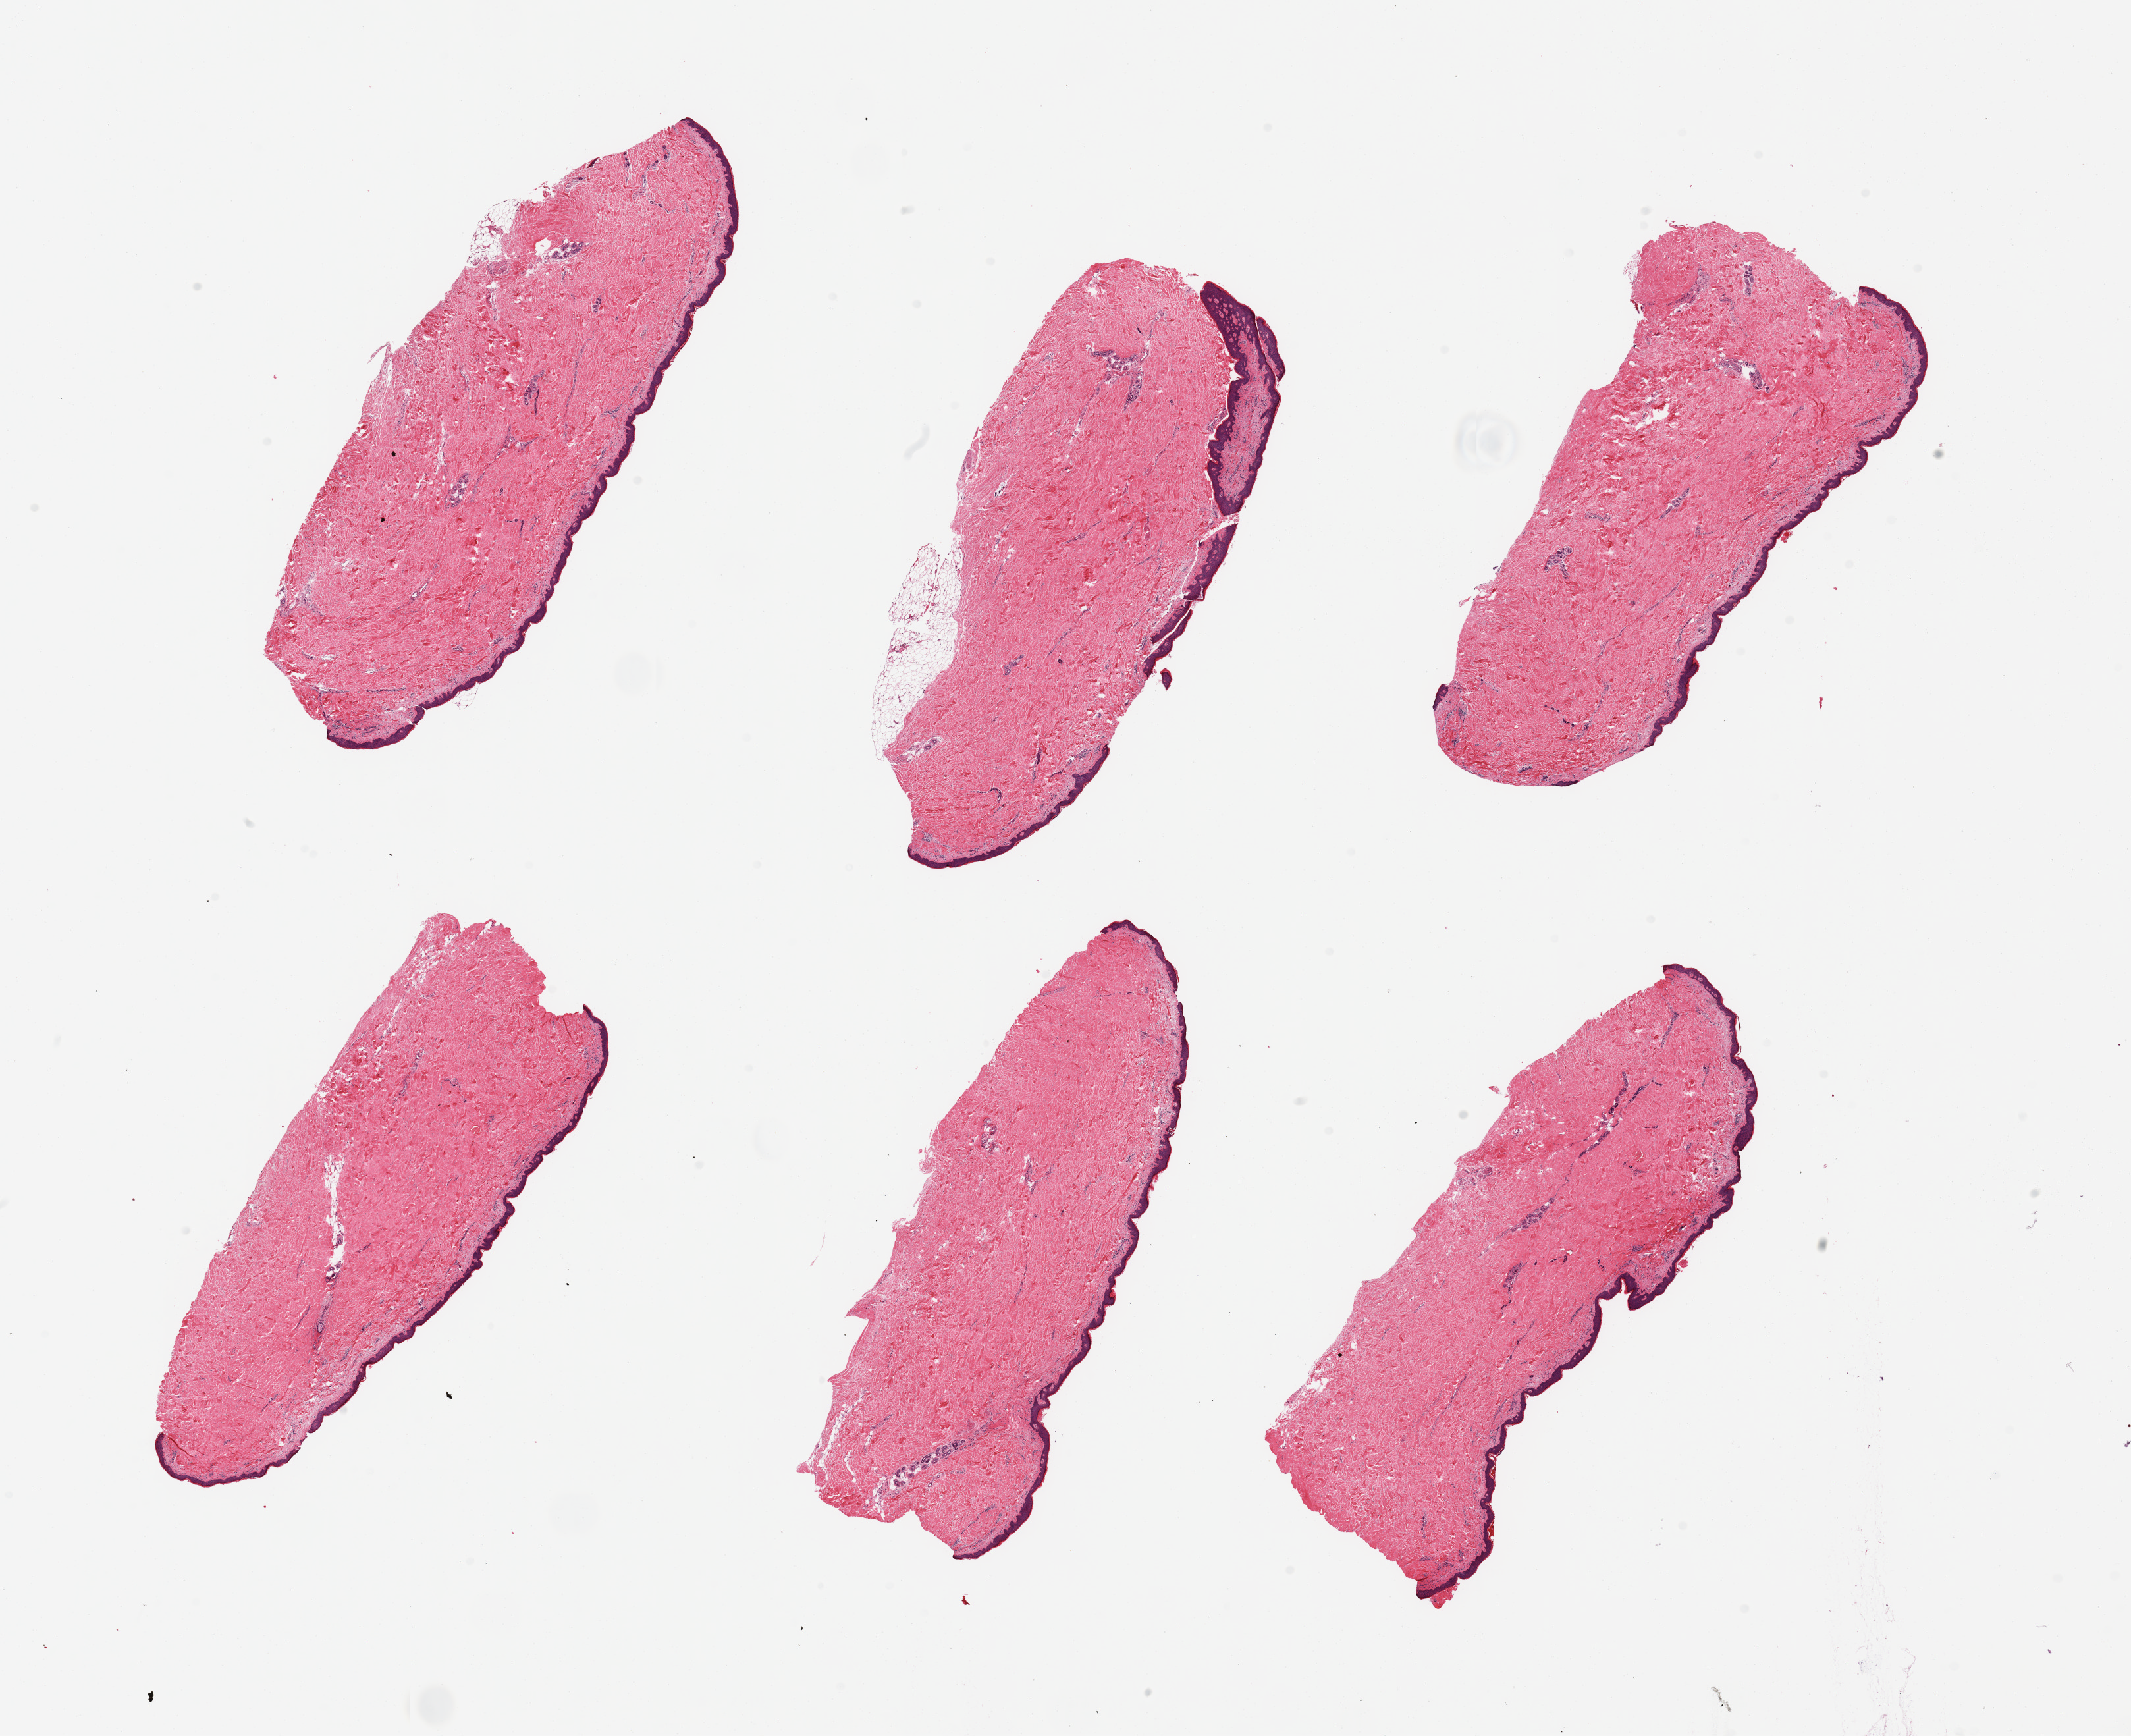
Digitized hematoxylin and eosin (H&E)-stained section, brightfield — whole scanned area (about 25.6 x 20.8 mm, slide scanned at 20x) shown as a low-resolution overview, PAXgene-fixed paraffin-embedded (PFPE) section, section of skin of suprapubic region (target tissue), tissue donor sample. Donor: male.
Pathologist's review note for this sample: 6 pieces; essentially well trimmed, small attachment of fat, 1 piece.